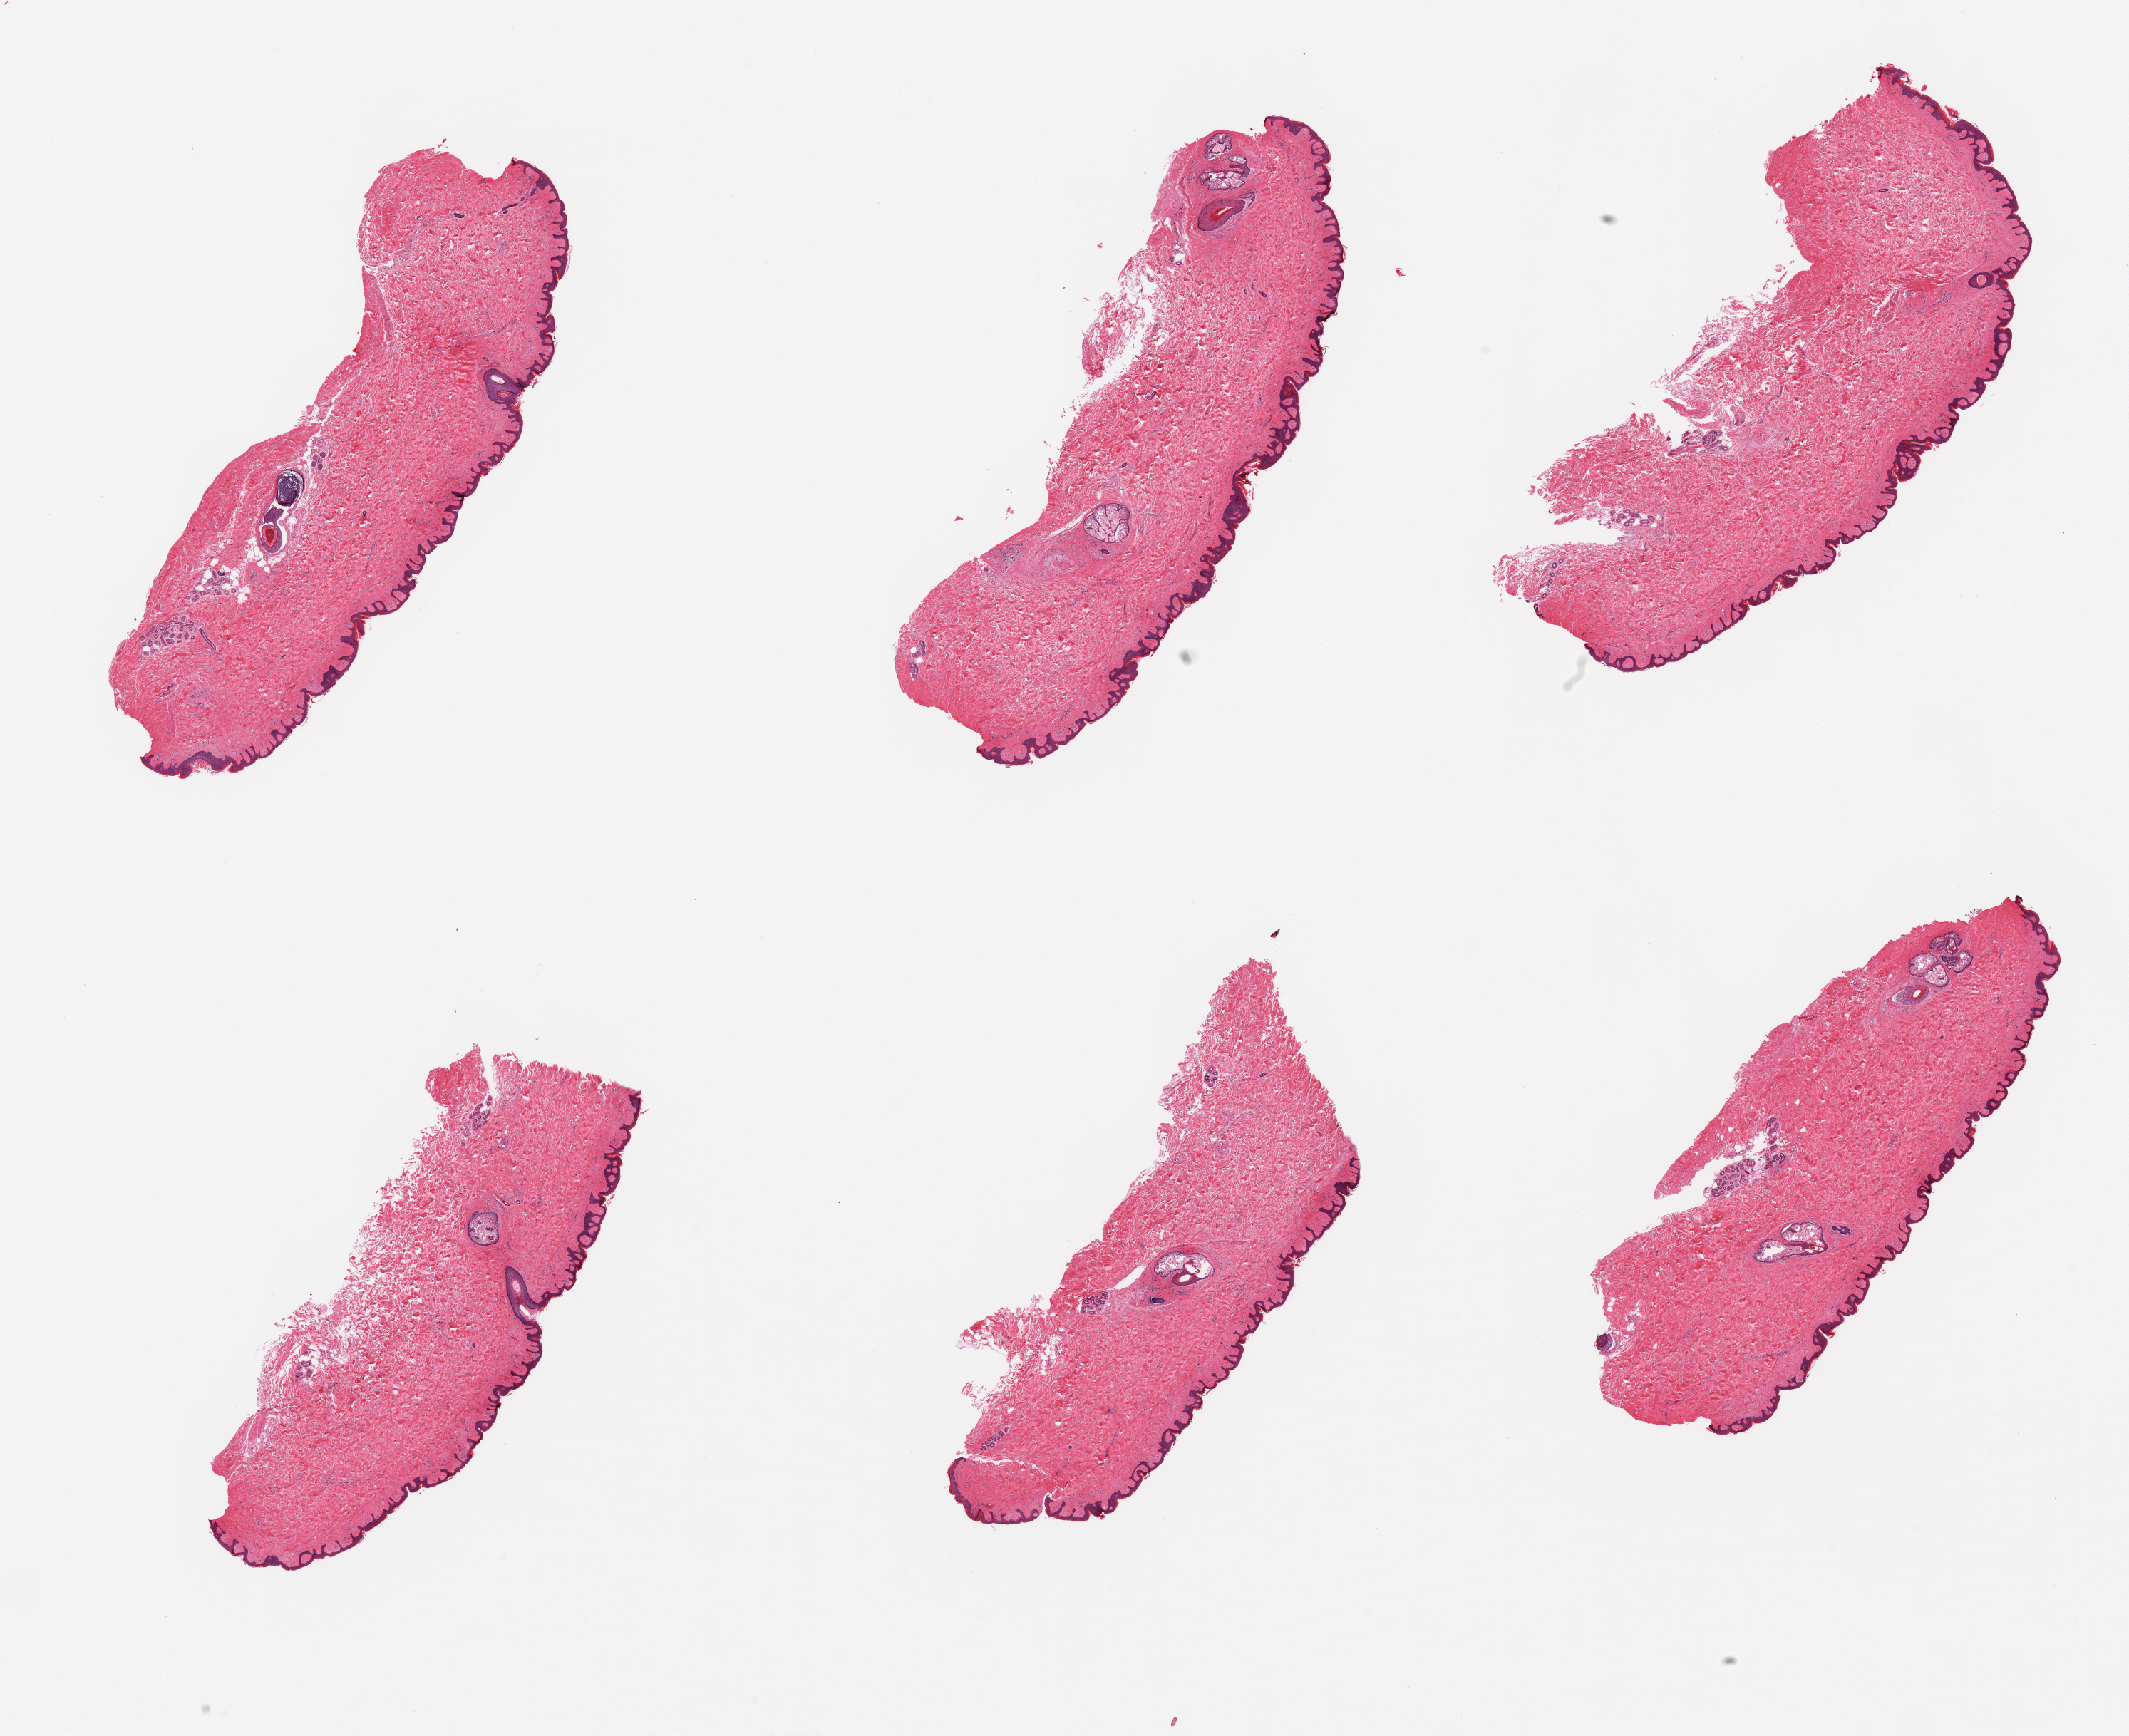
Haematoxylin and eosin whole-slide image, a low-resolution overview of the entire scanned area, about 23.6 x 19.3 mm (slide scanned at 20x), PAXgene-fixed, paraffin-embedded tissue, section of skin of suprapubic region (target tissue), tissue donor sample. Male donor.
- pathologist's review note for this sample: 6 pieces; thick collagen bands in deep dermis; virtually no dermal fat